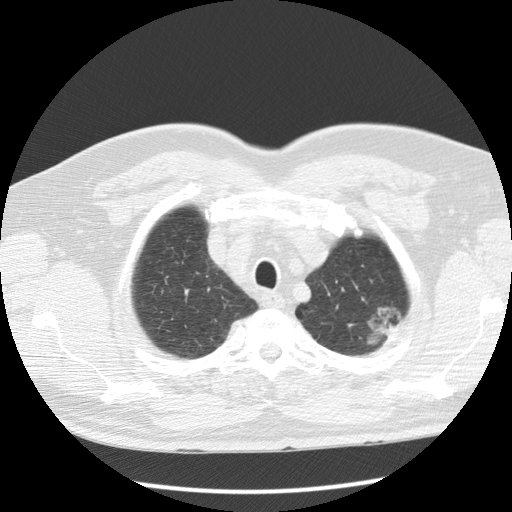
Chest CT (low-dose screening protocol), one axial image; first (baseline) screen; lung window (W 1500 / L -600 HU); 2.5 mm slice thickness; slice 16 of 123 in the series; 512 × 512 image matrix. Male participant, aged 60 years at enrolment. Current smoker at enrolment.
Expert reader's lesion annotation, bounding box <347,293,413,354> (left, top, right, bottom; pixels). The screening reader recorded 3 non-calcified nodules or masses ≥4 mm on this exam (left upper lobe, right upper lobe, left upper lobe); which of them this box marks is not recorded. Official screen result: positive, change unspecified: nodule(s) >= 4 mm or enlarging nodule(s), mass(es), or other non-specific abnormalities suspicious for lung cancer. Later outcome: lung cancer diagnosed 48 days after this screen — bronchiolo-alveolar adenocarcinoma, NOS, left upper lobe, well differentiated (G1), stage IA (AJCC 6th edition), 27 mm at pathology.